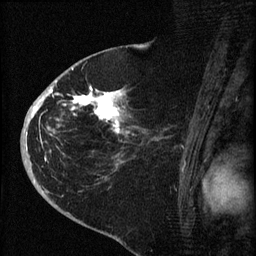
Breast MRI (dynamic contrast-enhanced), one sagittal slice. Slice 39 of 60 in the series (ordered by position). Dynamic contrast-enhanced series, image 2 of 4 at this slice position (ordered by acquisition). 1.5 T. TE 4.2 ms, TR 8.2 ms. 2 mm slice thickness. 256 × 256 image matrix. Female patient, age 71 years.
Structures marked on this image (semi-automatically segmented with operator editing):
- analysis volume of interest (the breast-tissue region the enhancement analysis was run in; not a lesion): box from (x=35, y=75) to (x=153, y=190) px
- tumour enhancement mask (voxels above the 70 % enhancement threshold inside the analysis volume of interest): (x=35, y=86)–(x=125, y=134)